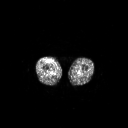
FDG PET of an extremity soft-tissue mass (from a PET/CT study), one axial slice; position 228 of 311 along the scan axis; 128 × 128 image matrix, field of view 700 × 700 mm. Male patient, age 56 years. From the clinical record (not read from this slice): histological type: pleiomorphic leiomyosarcoma; grade: intermediate; site of the primary tumour: right thigh.
Outlined on this slice (expert contour drawn on MRI and transferred to this co-registered scan by the dataset authors):
- gross tumour volume including surrounding oedema: box from (x=46, y=59) to (x=51, y=63) px